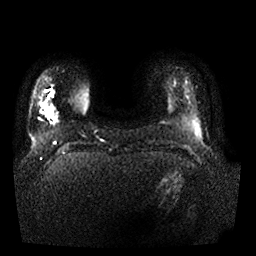
Breast MRI, one axial slice; slice 3 of 25 in the series (ordered by position); diffusion-weighted series; image 2 of 4 stored at this slice position (different b-values; order by instance number); 1.5 T; 4 mm slice thickness; 256 × 256 image matrix, field of view 350 × 350 mm. Female patient.
Annotated regions visible in this slice (manually delineated by an expert):
- tumour on diffusion-weighted imaging: bounding box (x1, y1, x2, y2) in pixels: (46, 108, 54, 119)